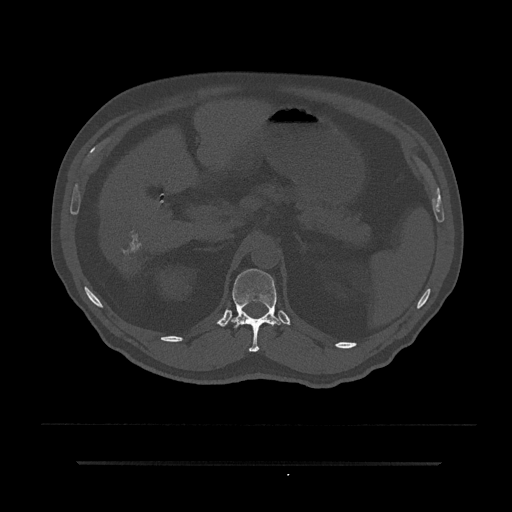
CT including the spine, one axial slice; position 209 of 797 along the scan axis; reconstruction kernel Br40s/3; 120 kVp; bone window (W 1800 / L 400 HU); 0.5 mm slice thickness; 512 × 512 image matrix, field of view 464 × 464 mm. Male patient, age 59 years. From the clinical record (not read from this slice): primary cancer: bile ducts.
Structures marked on this image (semi-automatically segmented with operator editing):
- T12 vertebra: box from (x=231, y=269) to (x=282, y=352) px